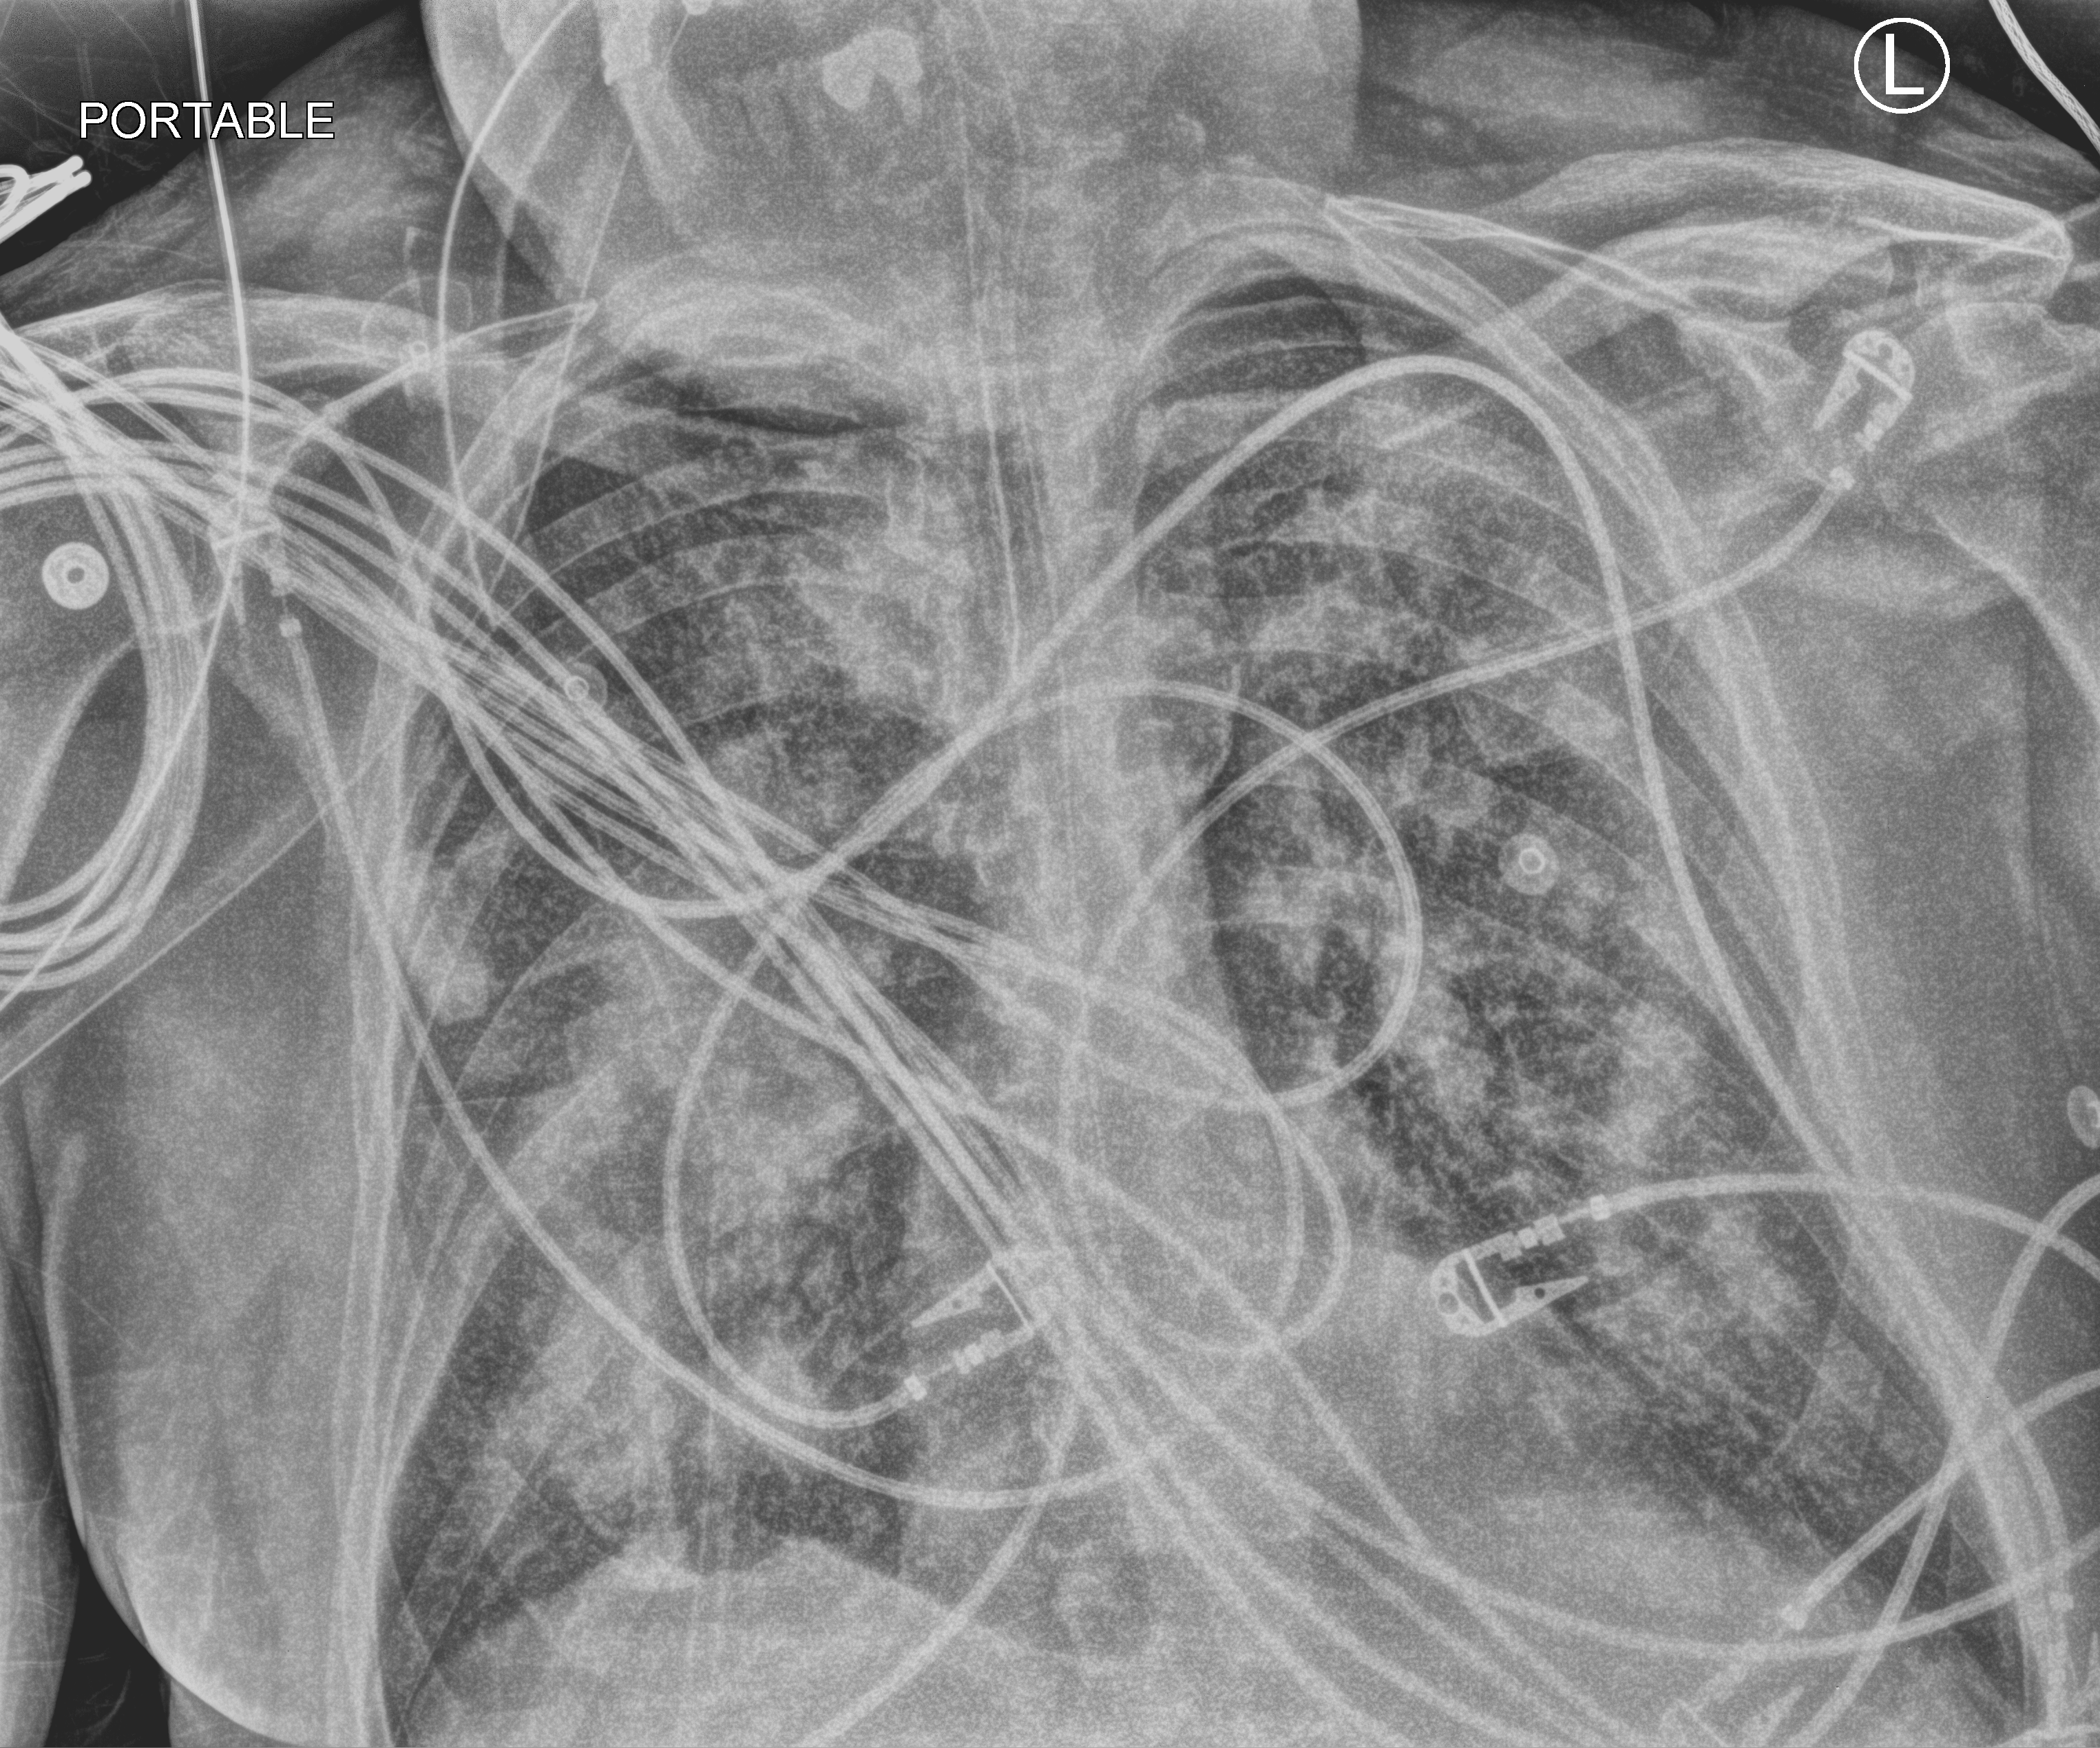
Chest X-ray (portable), anteroposterior (AP) projection. Male patient hospitalised with COVID-19, age 60–74 years.
Admission-level facts for this patient (not findings on this image; timing relative to this image not recorded): admitted to intensive care during this hospital stay: yes; length of hospital stay: 6 days; mechanically ventilated during this hospital stay: yes.